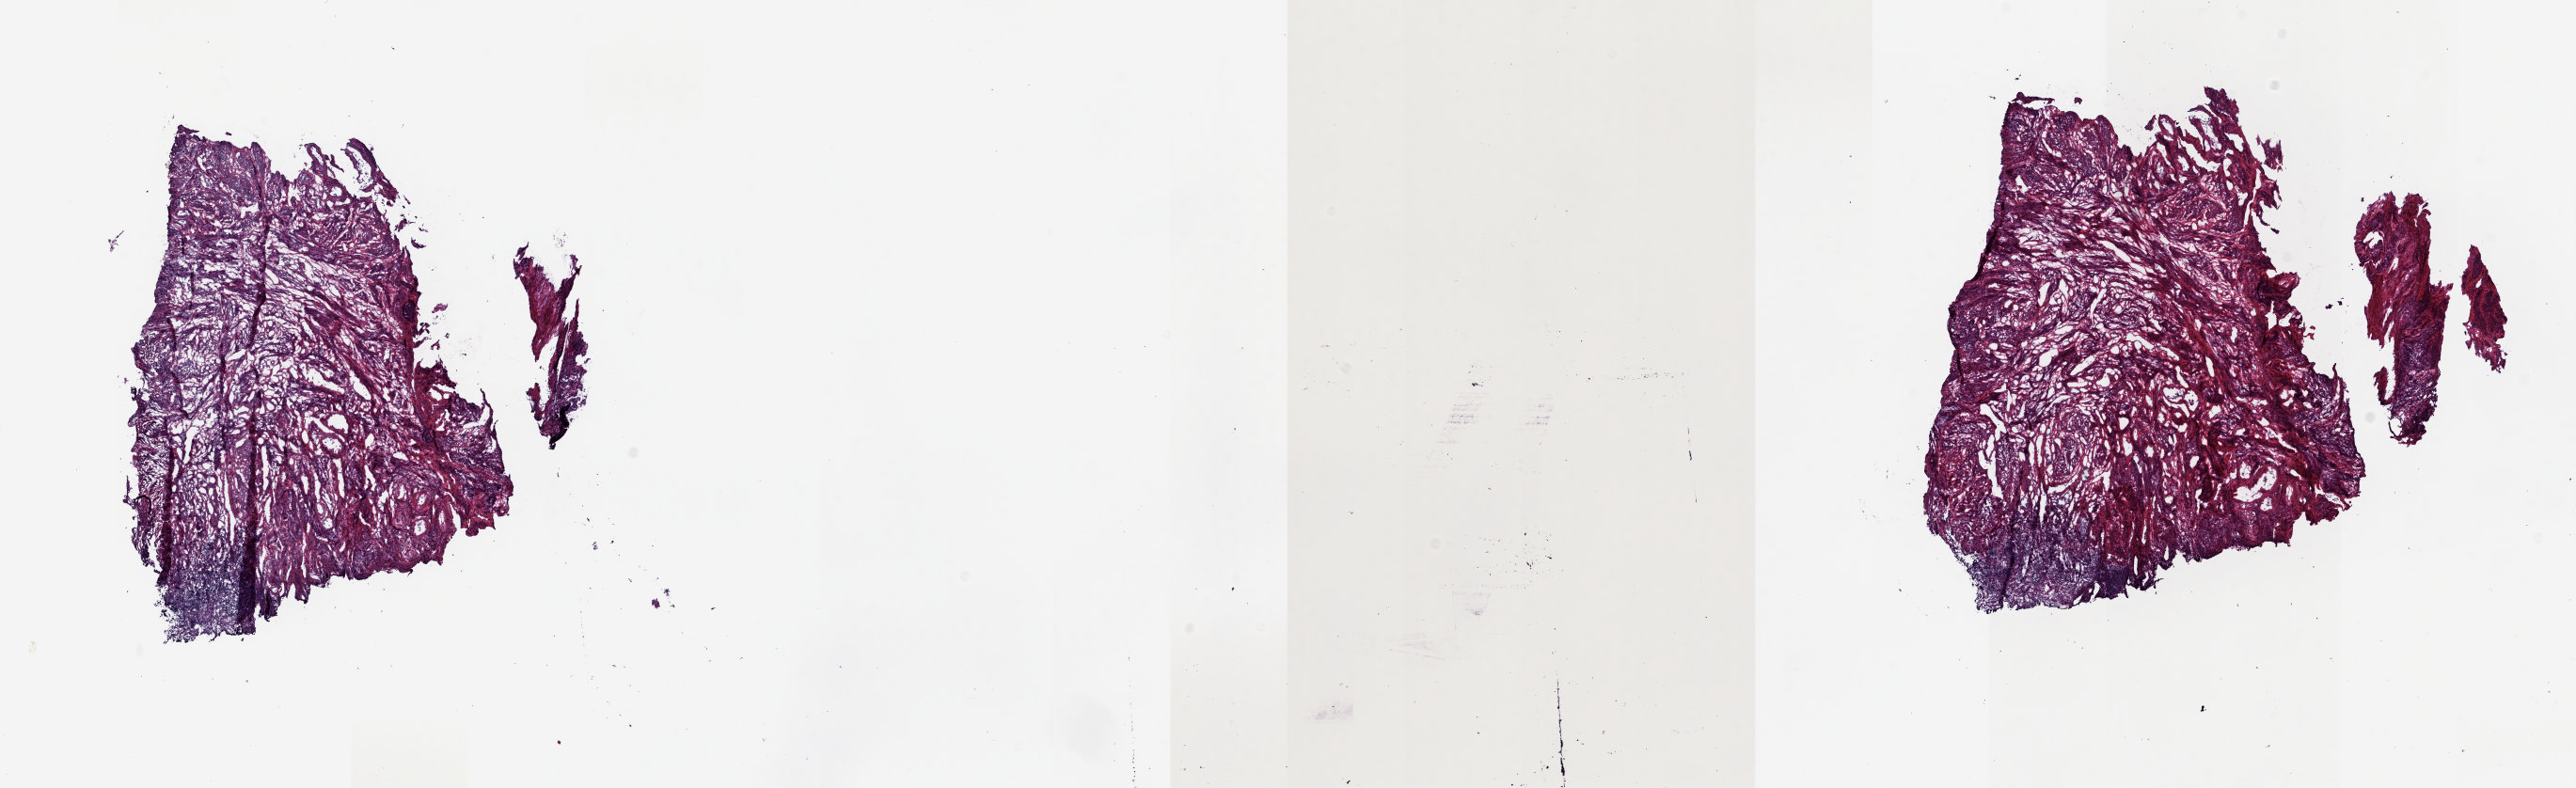
Digitized Hematoxylin and eosin (H&E) stained tissue section (whole slide) — a low-resolution overview of the entire scanned area, about 21.8 x 6.7 mm. Frozen section. Sample: solid tissue normal (non-tumour tissue), uterus. Slide review estimates, as recorded: tumour cells 0%, normal cells 100%.
This section: solid tissue normal (non-tumour) sample.